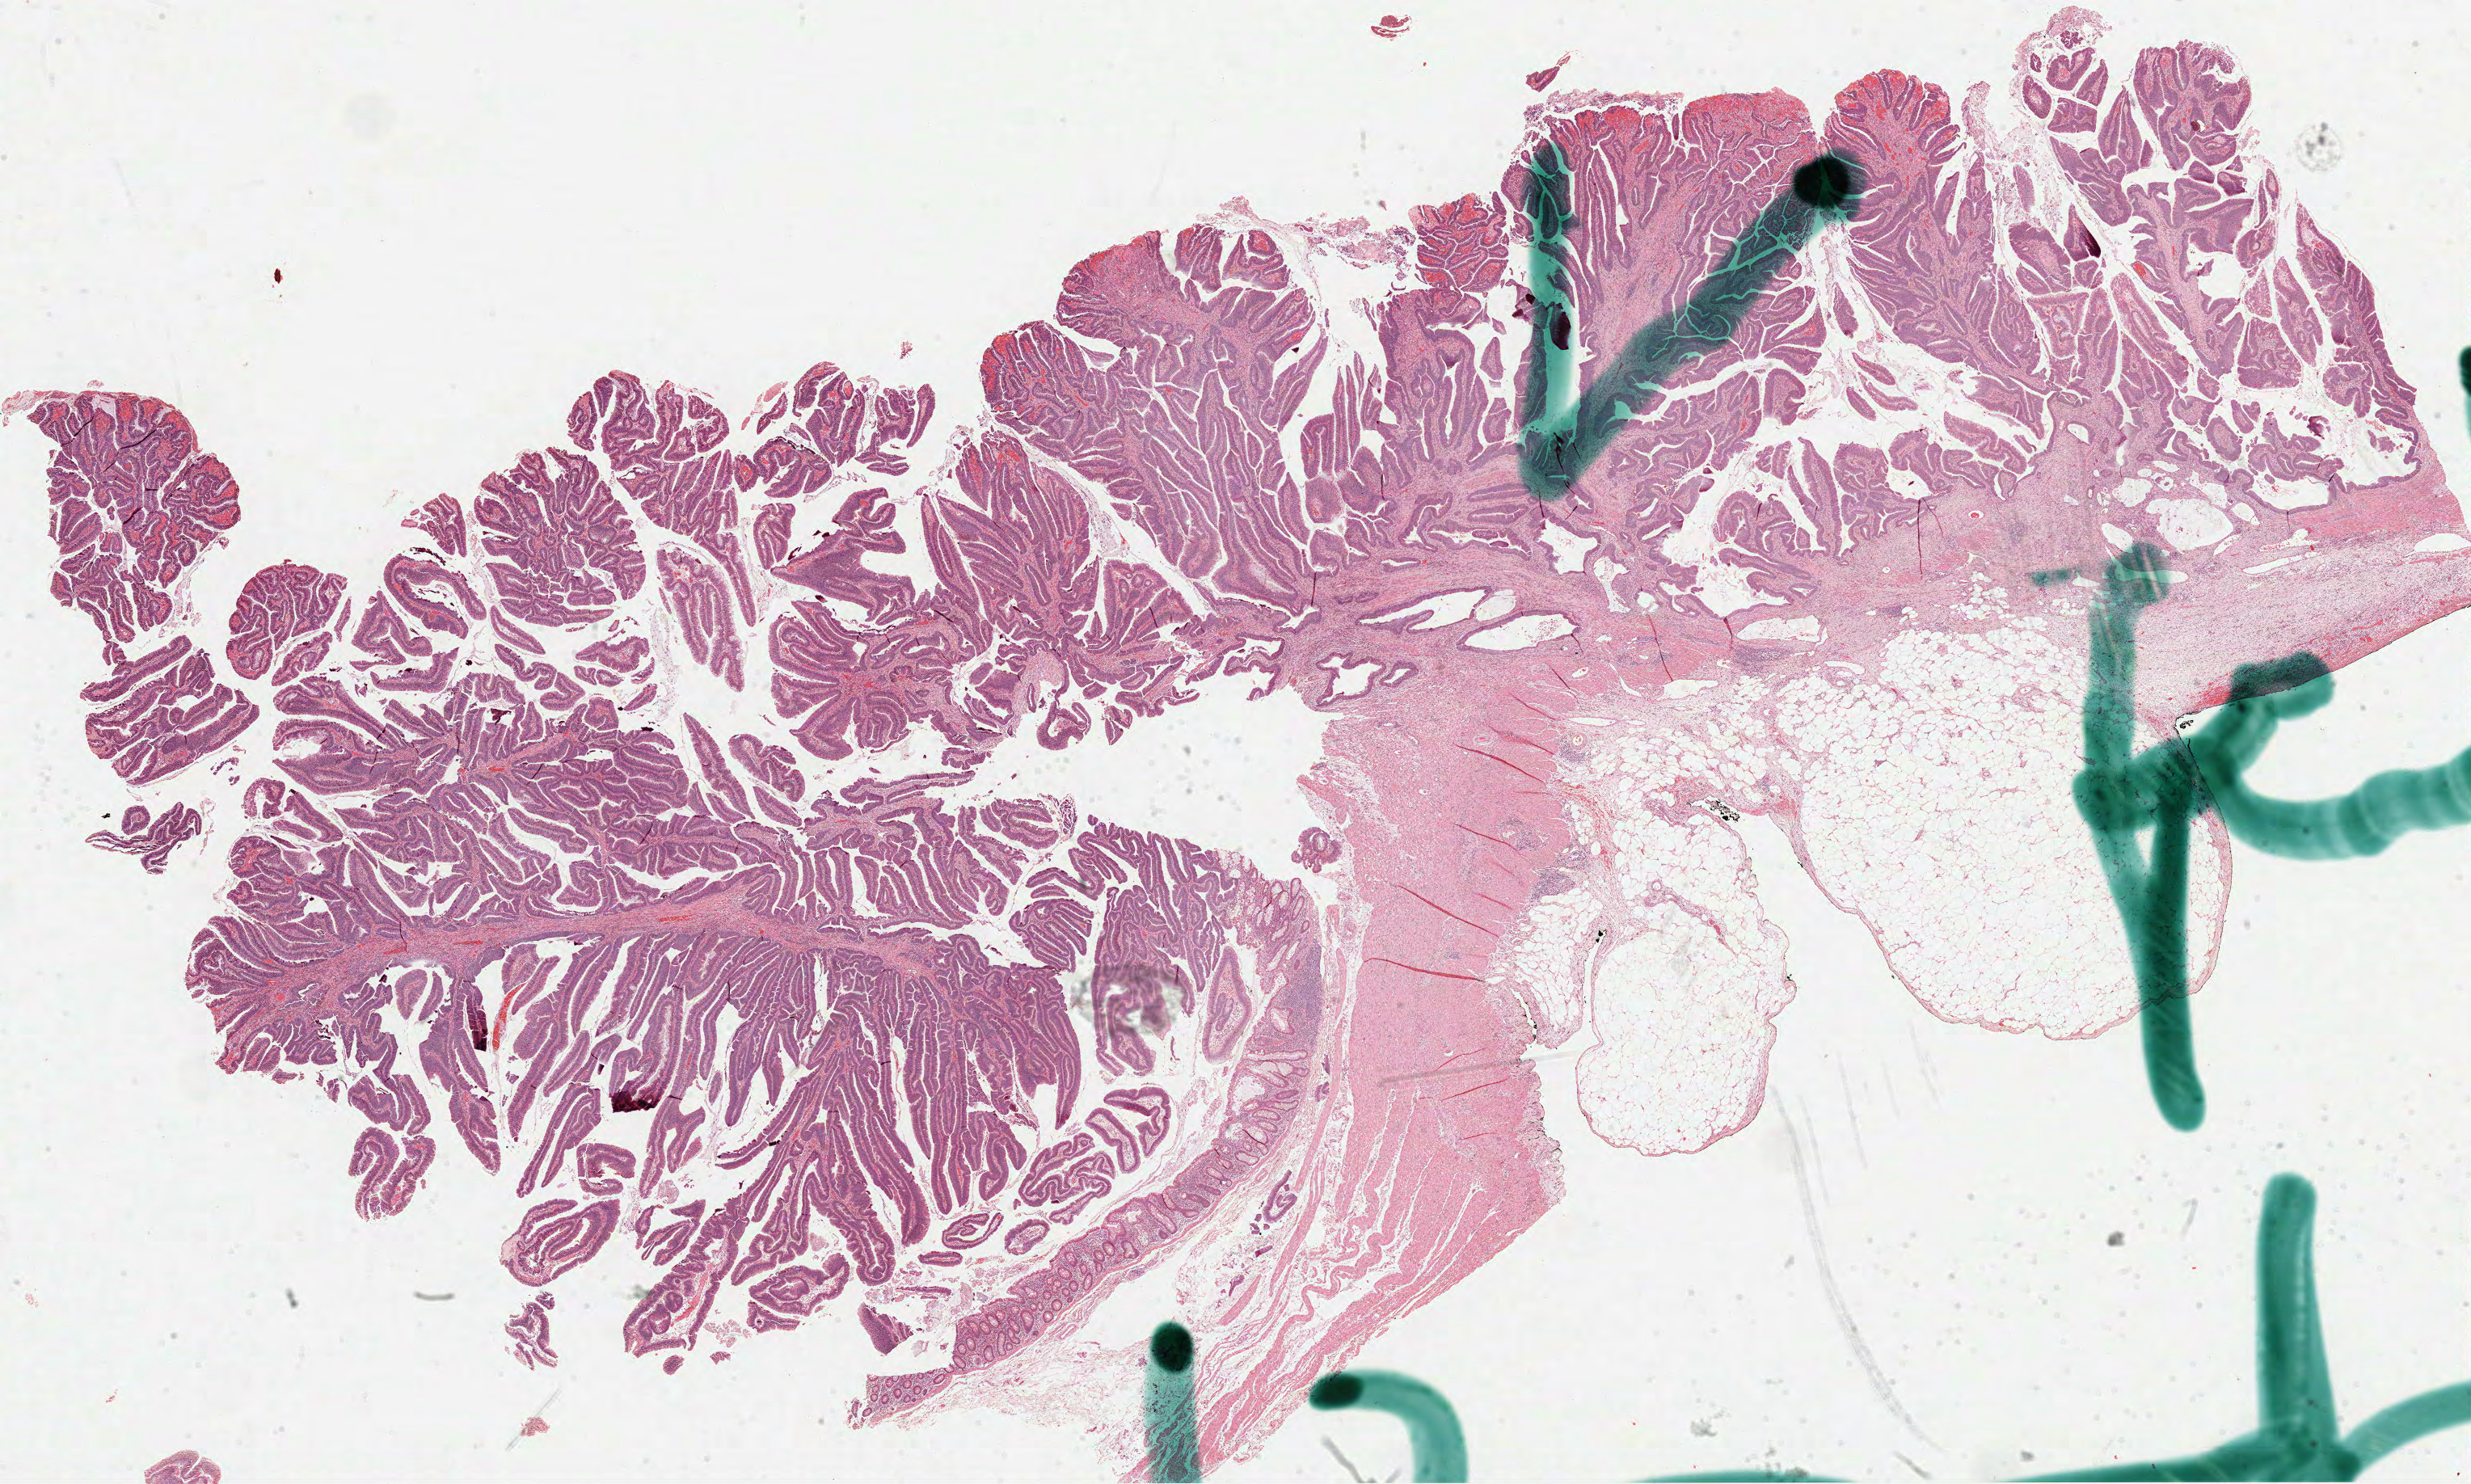
Whole-slide histology image, H&E — whole scanned area (about 24.7 x 14.8 mm, slide scanned at 40x) shown as a low-resolution overview. Formalin-fixed paraffin-embedded (FFPE) diagnostic section. Primary tumour sample from the colon. Male, age 72 years at initial diagnosis.
Pathologic diagnosis: Adenocarcinoma, NOS. AJCC pathologic stage: I. Lymph nodes positive (case pathology): 0 of 25 examined.